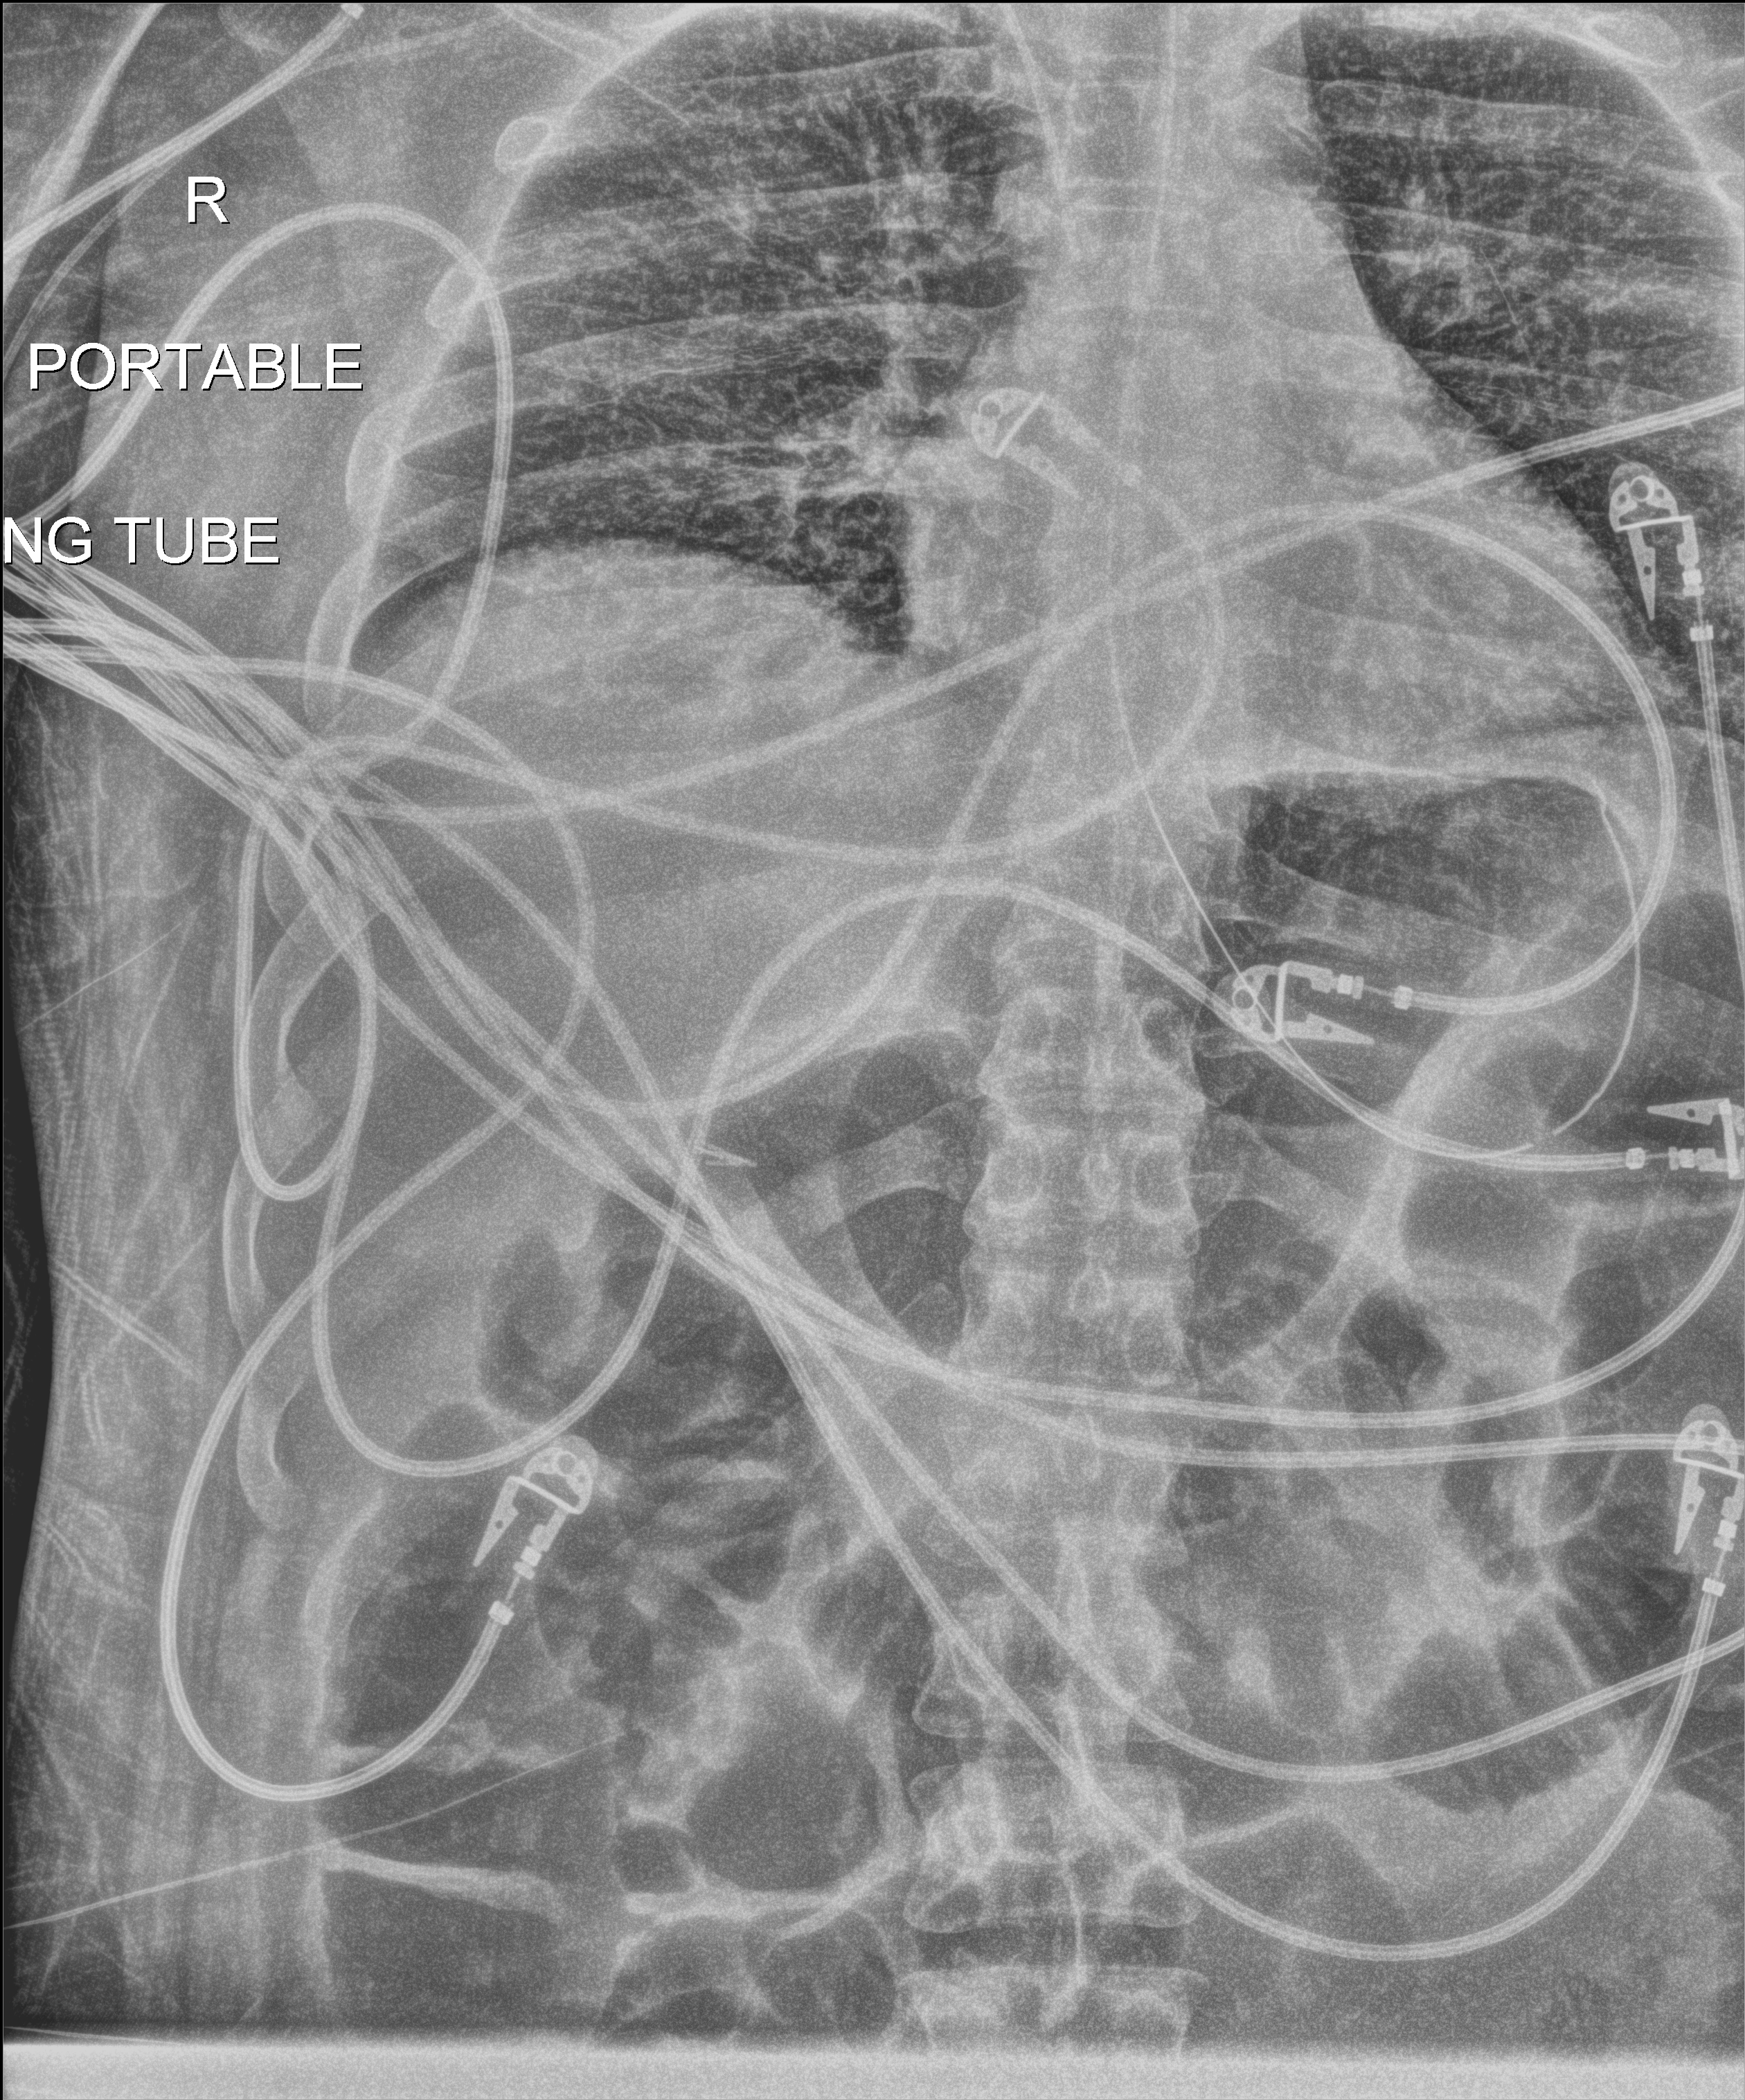
Portable chest radiograph, anteroposterior (AP) projection. Patient hospitalised with COVID-19; male, aged 18–59 years.
Hospital-stay facts (about this admission, not read from this image; timing relative to this image not recorded):
- admitted to intensive care during this hospital stay: yes